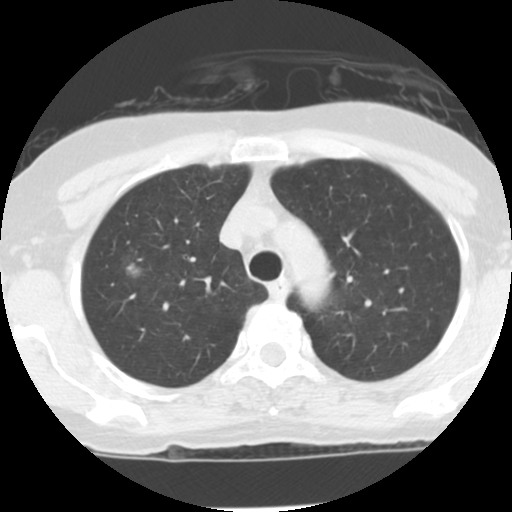
Axial slice from a low-dose chest CT screening exam, third screening round (two years after baseline), lung window (W 1500 / L -600 HU), 2.5 mm slice thickness, slice 26 of 122 in the series. Female, age 62 years at enrolment. Current smoker at enrolment.
Lesion marked by an expert reader, box from (x=110, y=247) to (x=158, y=293) px. Screening reader's record for this exam (one nodule recorded; not confirmed to be the boxed lesion): non-calcified nodule or mass ≥4 mm, right upper lobe, 9 × 8 mm, poorly defined margins, ground glass attenuation, pre-existing on the prior screen: yes; interval growth: yes. Official screen result: positive, other. Participant outcome: lung cancer diagnosed 134 days after this screen — bronchiolo-alveolar adenocarcinoma, NOS, right upper lobe, stage IA (AJCC 6th edition), 10 mm at pathology.